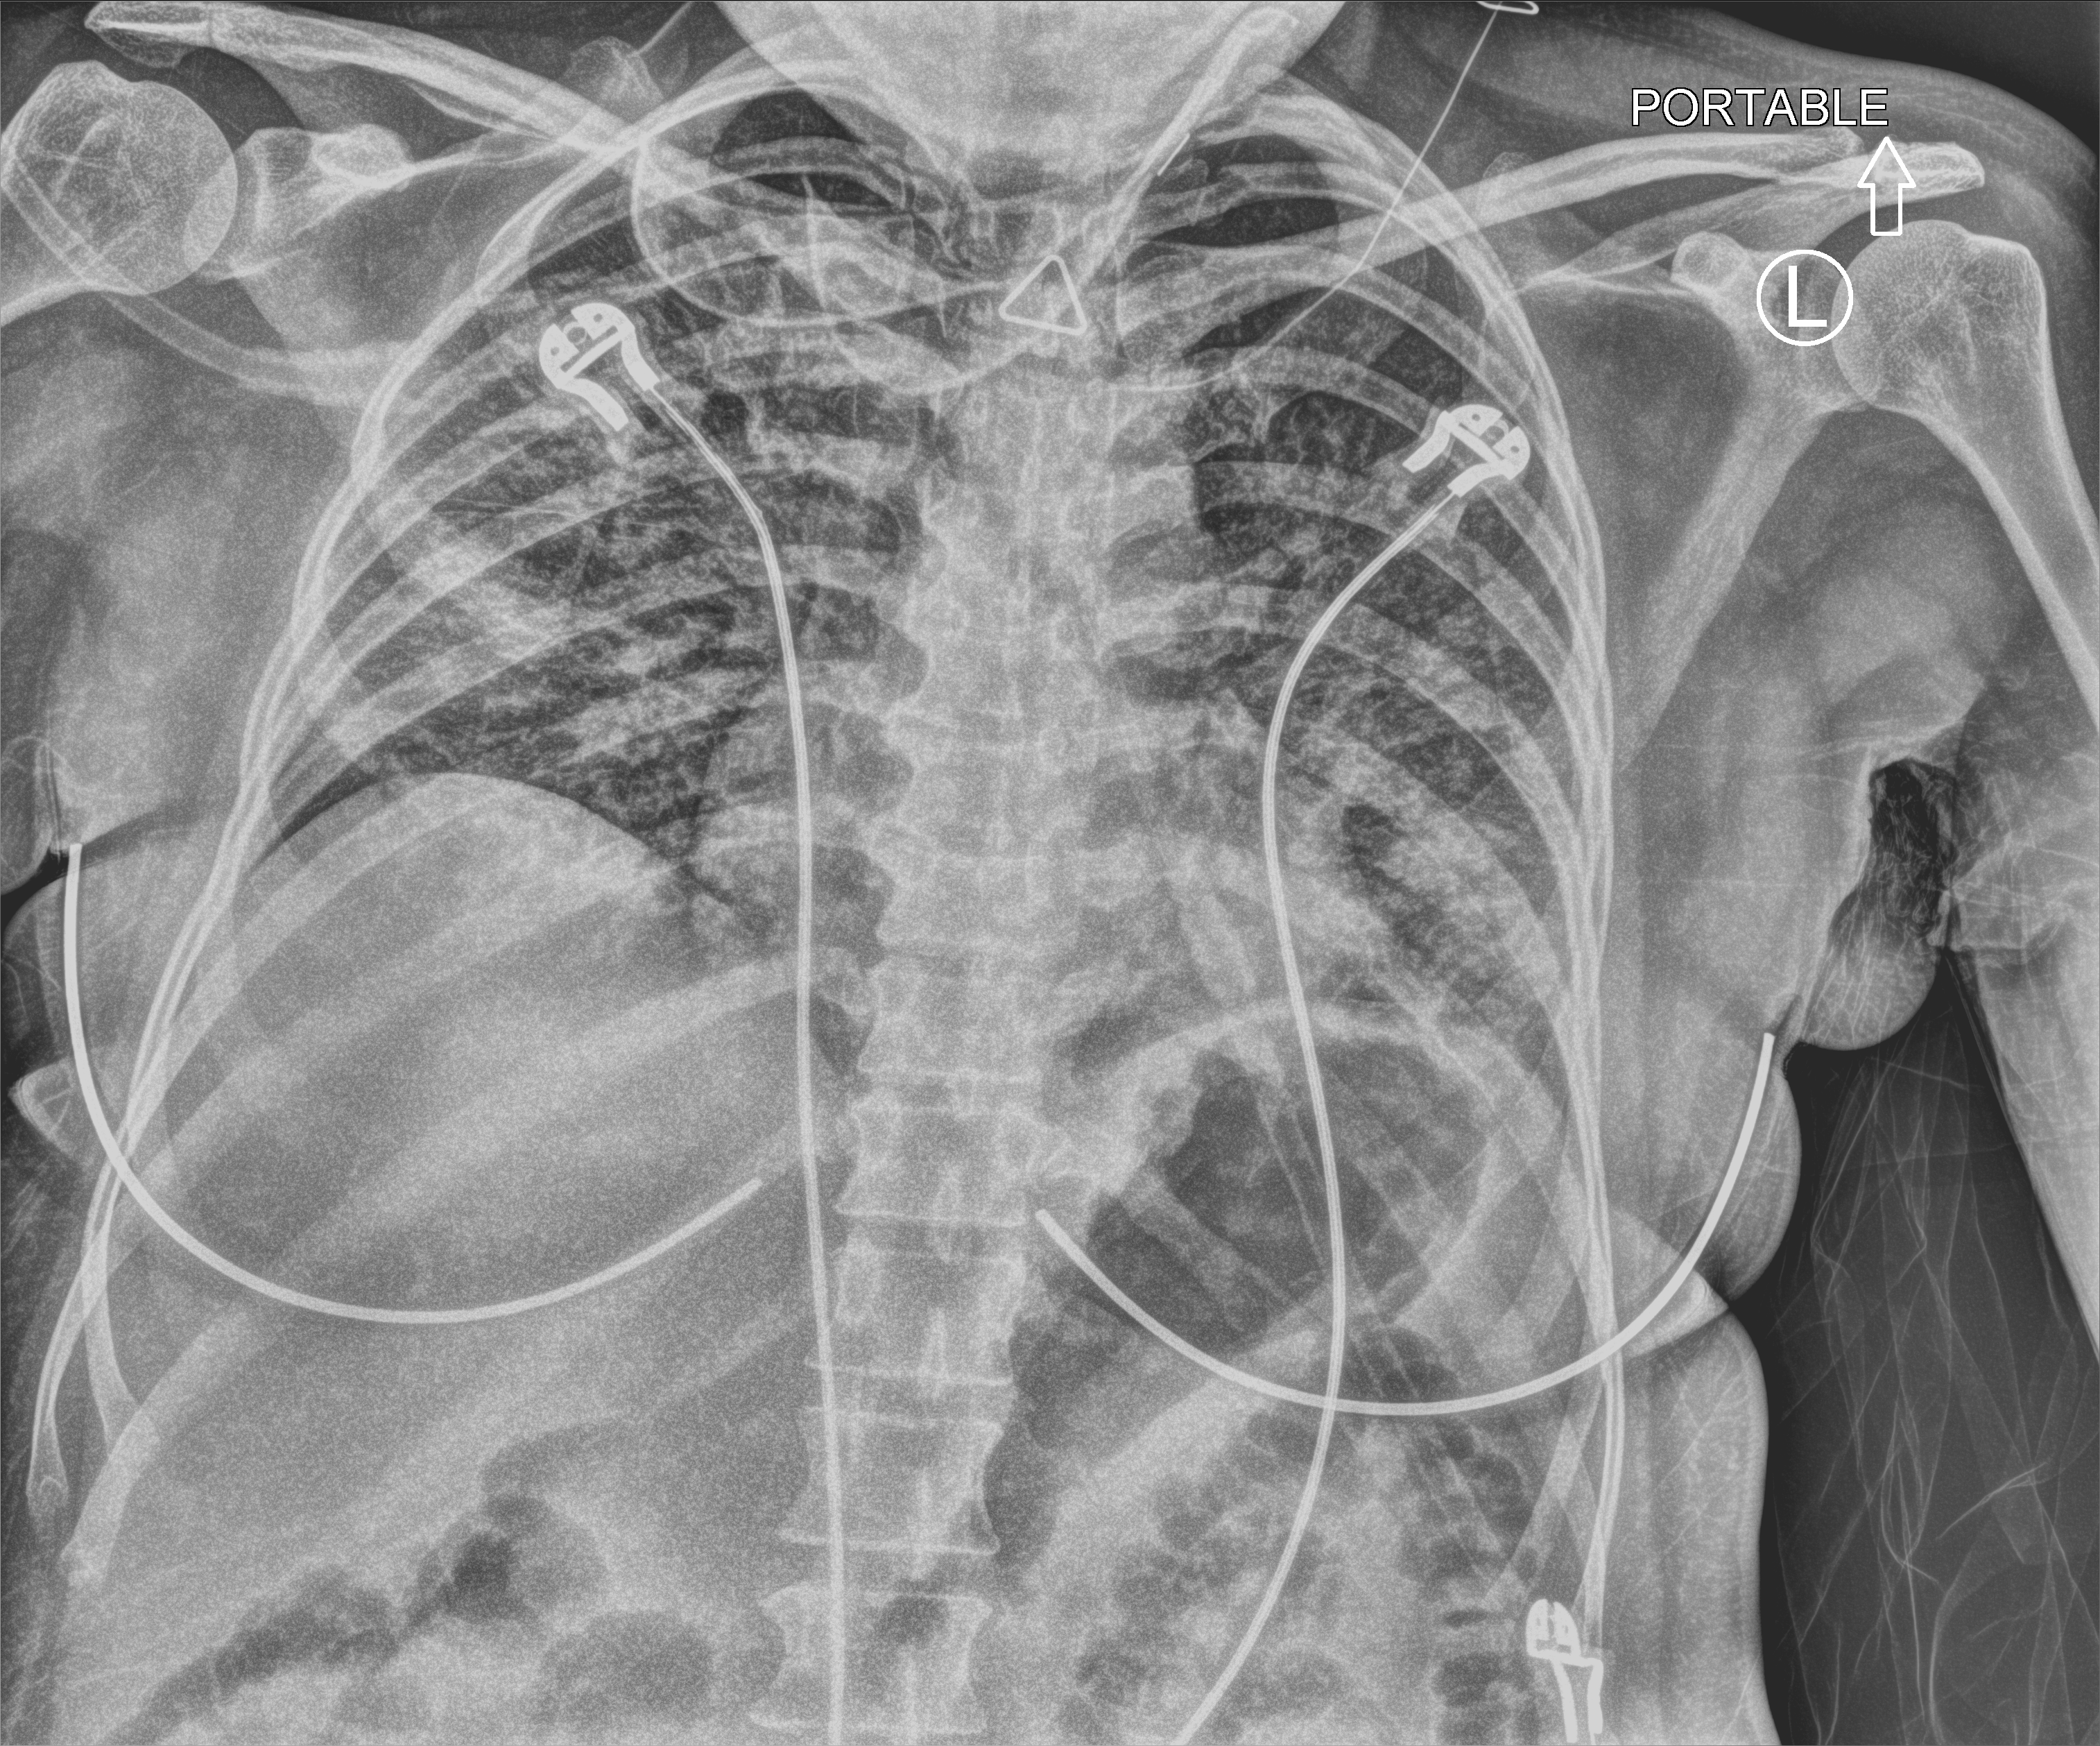
Chest X-ray (portable), anteroposterior (AP) projection. Patient hospitalised with COVID-19; female, aged 18–59 years.
Hospital-stay facts (about this admission, not read from this image; timing relative to this image not recorded):
- diabetes (admission record): no